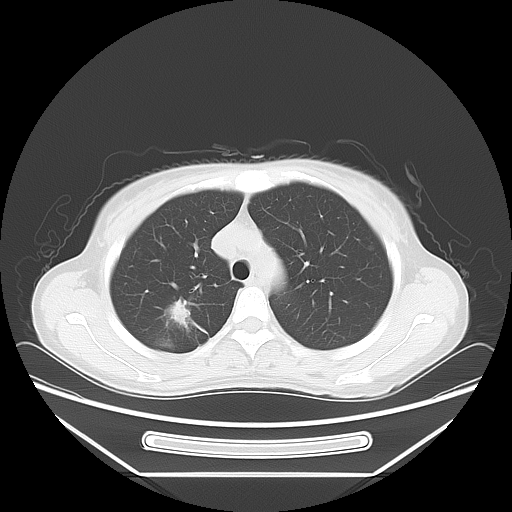
Chest CT, one axial slice. Slice 50 of 66 in the series (ordered by position). Reconstruction kernel LUNG. Lung window (W 1500 / L -600 HU). 5 mm slice thickness. 512 × 512 image matrix, field of view 408 × 408 mm. Female patient, age 37 years. Case-level facts recorded for this patient, not image findings: clinical TNM (as recorded): T1c N0 M1.
Structures marked on this image (rectangle marked by the reading radiologist):
- lung tumour (recorded histology: adenocarcinoma): bounding box (x1, y1, x2, y2) in pixels: (161, 291, 196, 330)